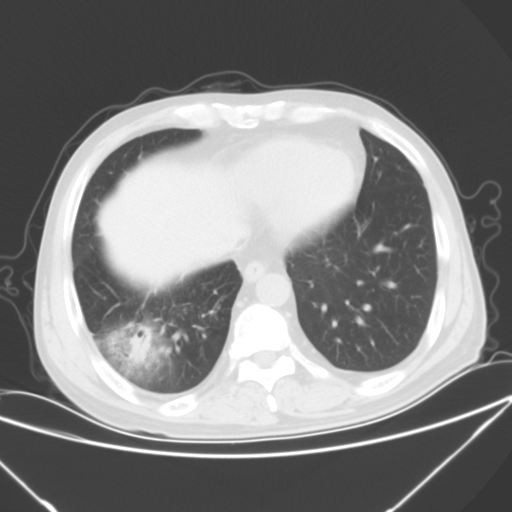
Chest CT, one axial slice; position 19 of 57 along the scan axis; 120 kVp; lung window (W 1500 / L -600 HU); 5 mm slice thickness; 512 × 512 image matrix, field of view 364 × 364 mm. Patient: male, 54 years. Case-level facts recorded for this patient, not image findings: clinical TNM (as recorded): T2 N1 M0; histopathological grade: G3.
Structures marked on this image (rectangle marked by the reading radiologist):
- lung tumour (recorded histology: adenocarcinoma): bounding box <130,327,151,362> (left, top, right, bottom; pixels)